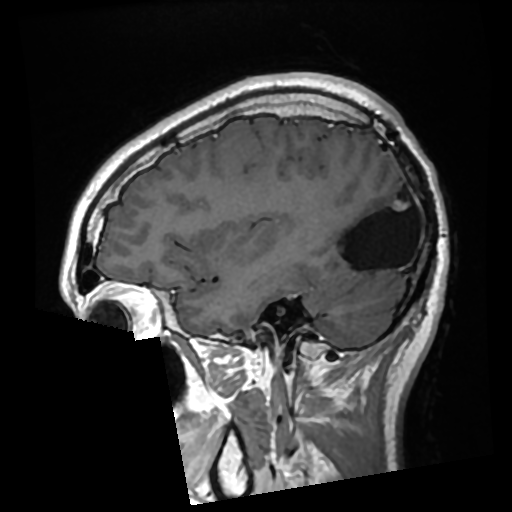
Brain MRI from a brain-tumour surgery series, one sagittal slice; slice 90 of 276 in the series (ordered by position); T1-weighted post-contrast; 0.7 mm slice thickness; 512 × 512 image matrix, field of view 250 × 250 mm. Case-level facts recorded for this patient, not image findings: histopathology: Glioma with ependymal features; WHO grade: 2.
Outlined on this slice (outlined manually by an expert reader):
- previous resection cavity: bounding box (x1, y1, x2, y2) in pixels: (333, 182, 412, 270)
- tumour: (393, 201, 408, 211)